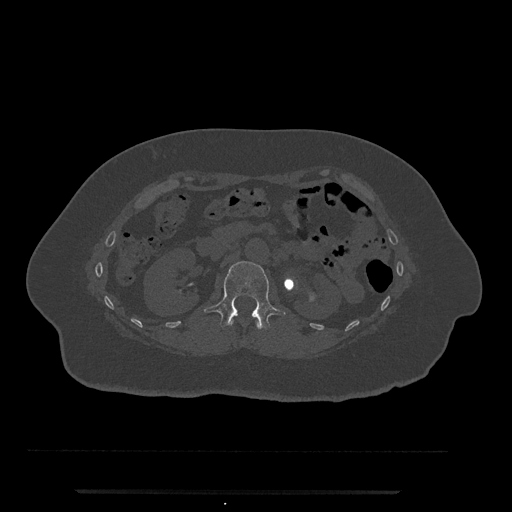
CT including the spine, one axial slice; position 114 of 797 along the scan axis; reconstruction kernel Br40s/3; 120 kVp; bone window (W 1800 / L 400 HU); 0.5 mm slice thickness; 512 × 512 image matrix. Female patient, age 51 years. Case-level facts recorded for this patient, not image findings: primary cancer: neuro.
Structures marked on this image (semi-automatic segmentation, software-assisted and operator-edited):
- L1 vertebra: bounding box [x1, y1, x2, y2] px = [204, 261, 286, 330]
- T12 vertebra: [230, 319, 261, 330]